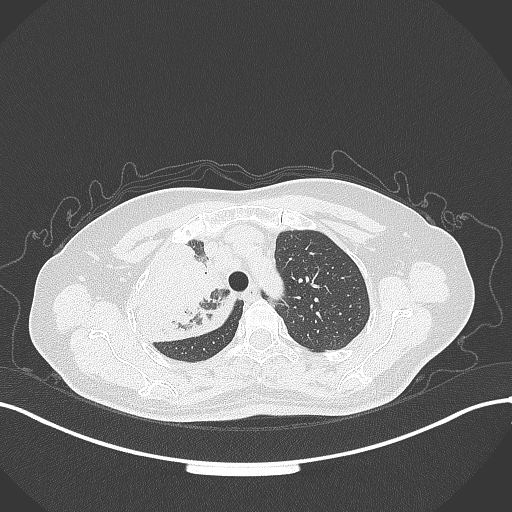
Chest CT, one axial slice; position 247 of 309 along the scan axis; reconstruction kernel B70f; lung window (W 1500 / L -600 HU); 512 × 512 image matrix, field of view 400 × 400 mm. Female patient, age 60 years. Case-level facts recorded for this patient, not image findings: clinical TNM (as recorded): T3 N1 M1.
Annotated regions visible in this slice (bounding box drawn by a radiologist):
- lung tumour (recorded histology: adenocarcinoma): bounding box <130,239,240,348> (left, top, right, bottom; pixels)